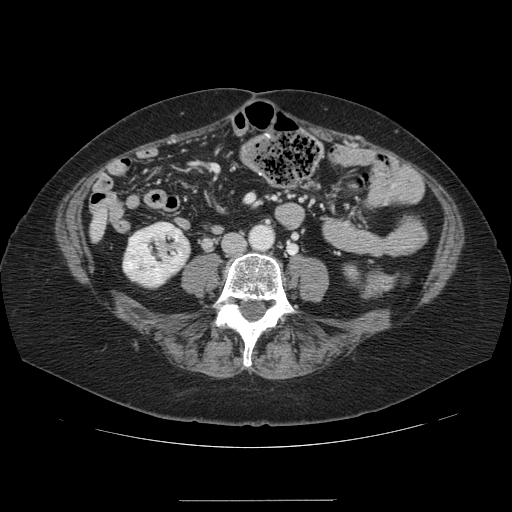
Contrast-enhanced abdominal CT, one axial slice. Slice 9 of 141 in the series (ordered by position). 120 kVp. Intravenous contrast given. Soft-tissue window (W 400 / L 40 HU). 2.5 mm slice thickness. 512 × 512 image matrix, field of view 393 × 393 mm. Female patient, age 74 years. Case-level facts recorded for this patient, not image findings: diagnosis: colorectal cancer liver metastases, imaged before liver resection; multiple liver metastases: yes; largest metastasis: 7 cm.
Structures marked on this image (expert manual segmentation):
- liver: bounding box [x1, y1, x2, y2] px = [94, 214, 104, 237]
- planned liver remnant (the part of the liver to remain after resection): [96, 214, 104, 237]